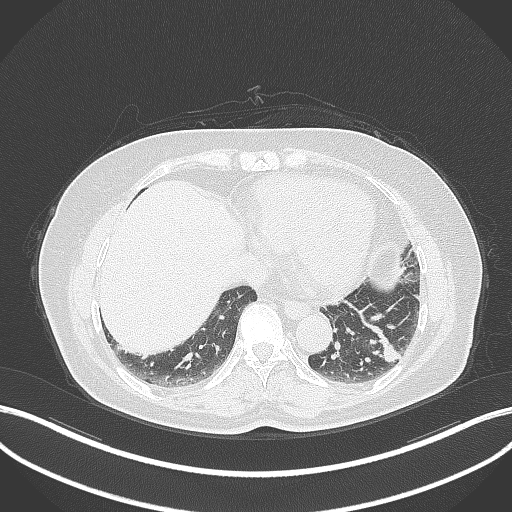
Chest CT, one axial slice. Slice 115 of 311 in the series (ordered by position). 120 kVp. Lung window (W 1500 / L -600 HU). 1 mm slice thickness. 512 × 512 image matrix, field of view 400 × 400 mm. Female patient, age 59 years. Case-level facts recorded for this patient, not image findings: clinical TNM (as recorded): T2a N0 M0; histopathological grade: G2-3.
Structures marked on this image (bounding box drawn by a radiologist):
- lung tumour (recorded histology: adenocarcinoma): bounding box [x1, y1, x2, y2] px = [373, 325, 410, 369]